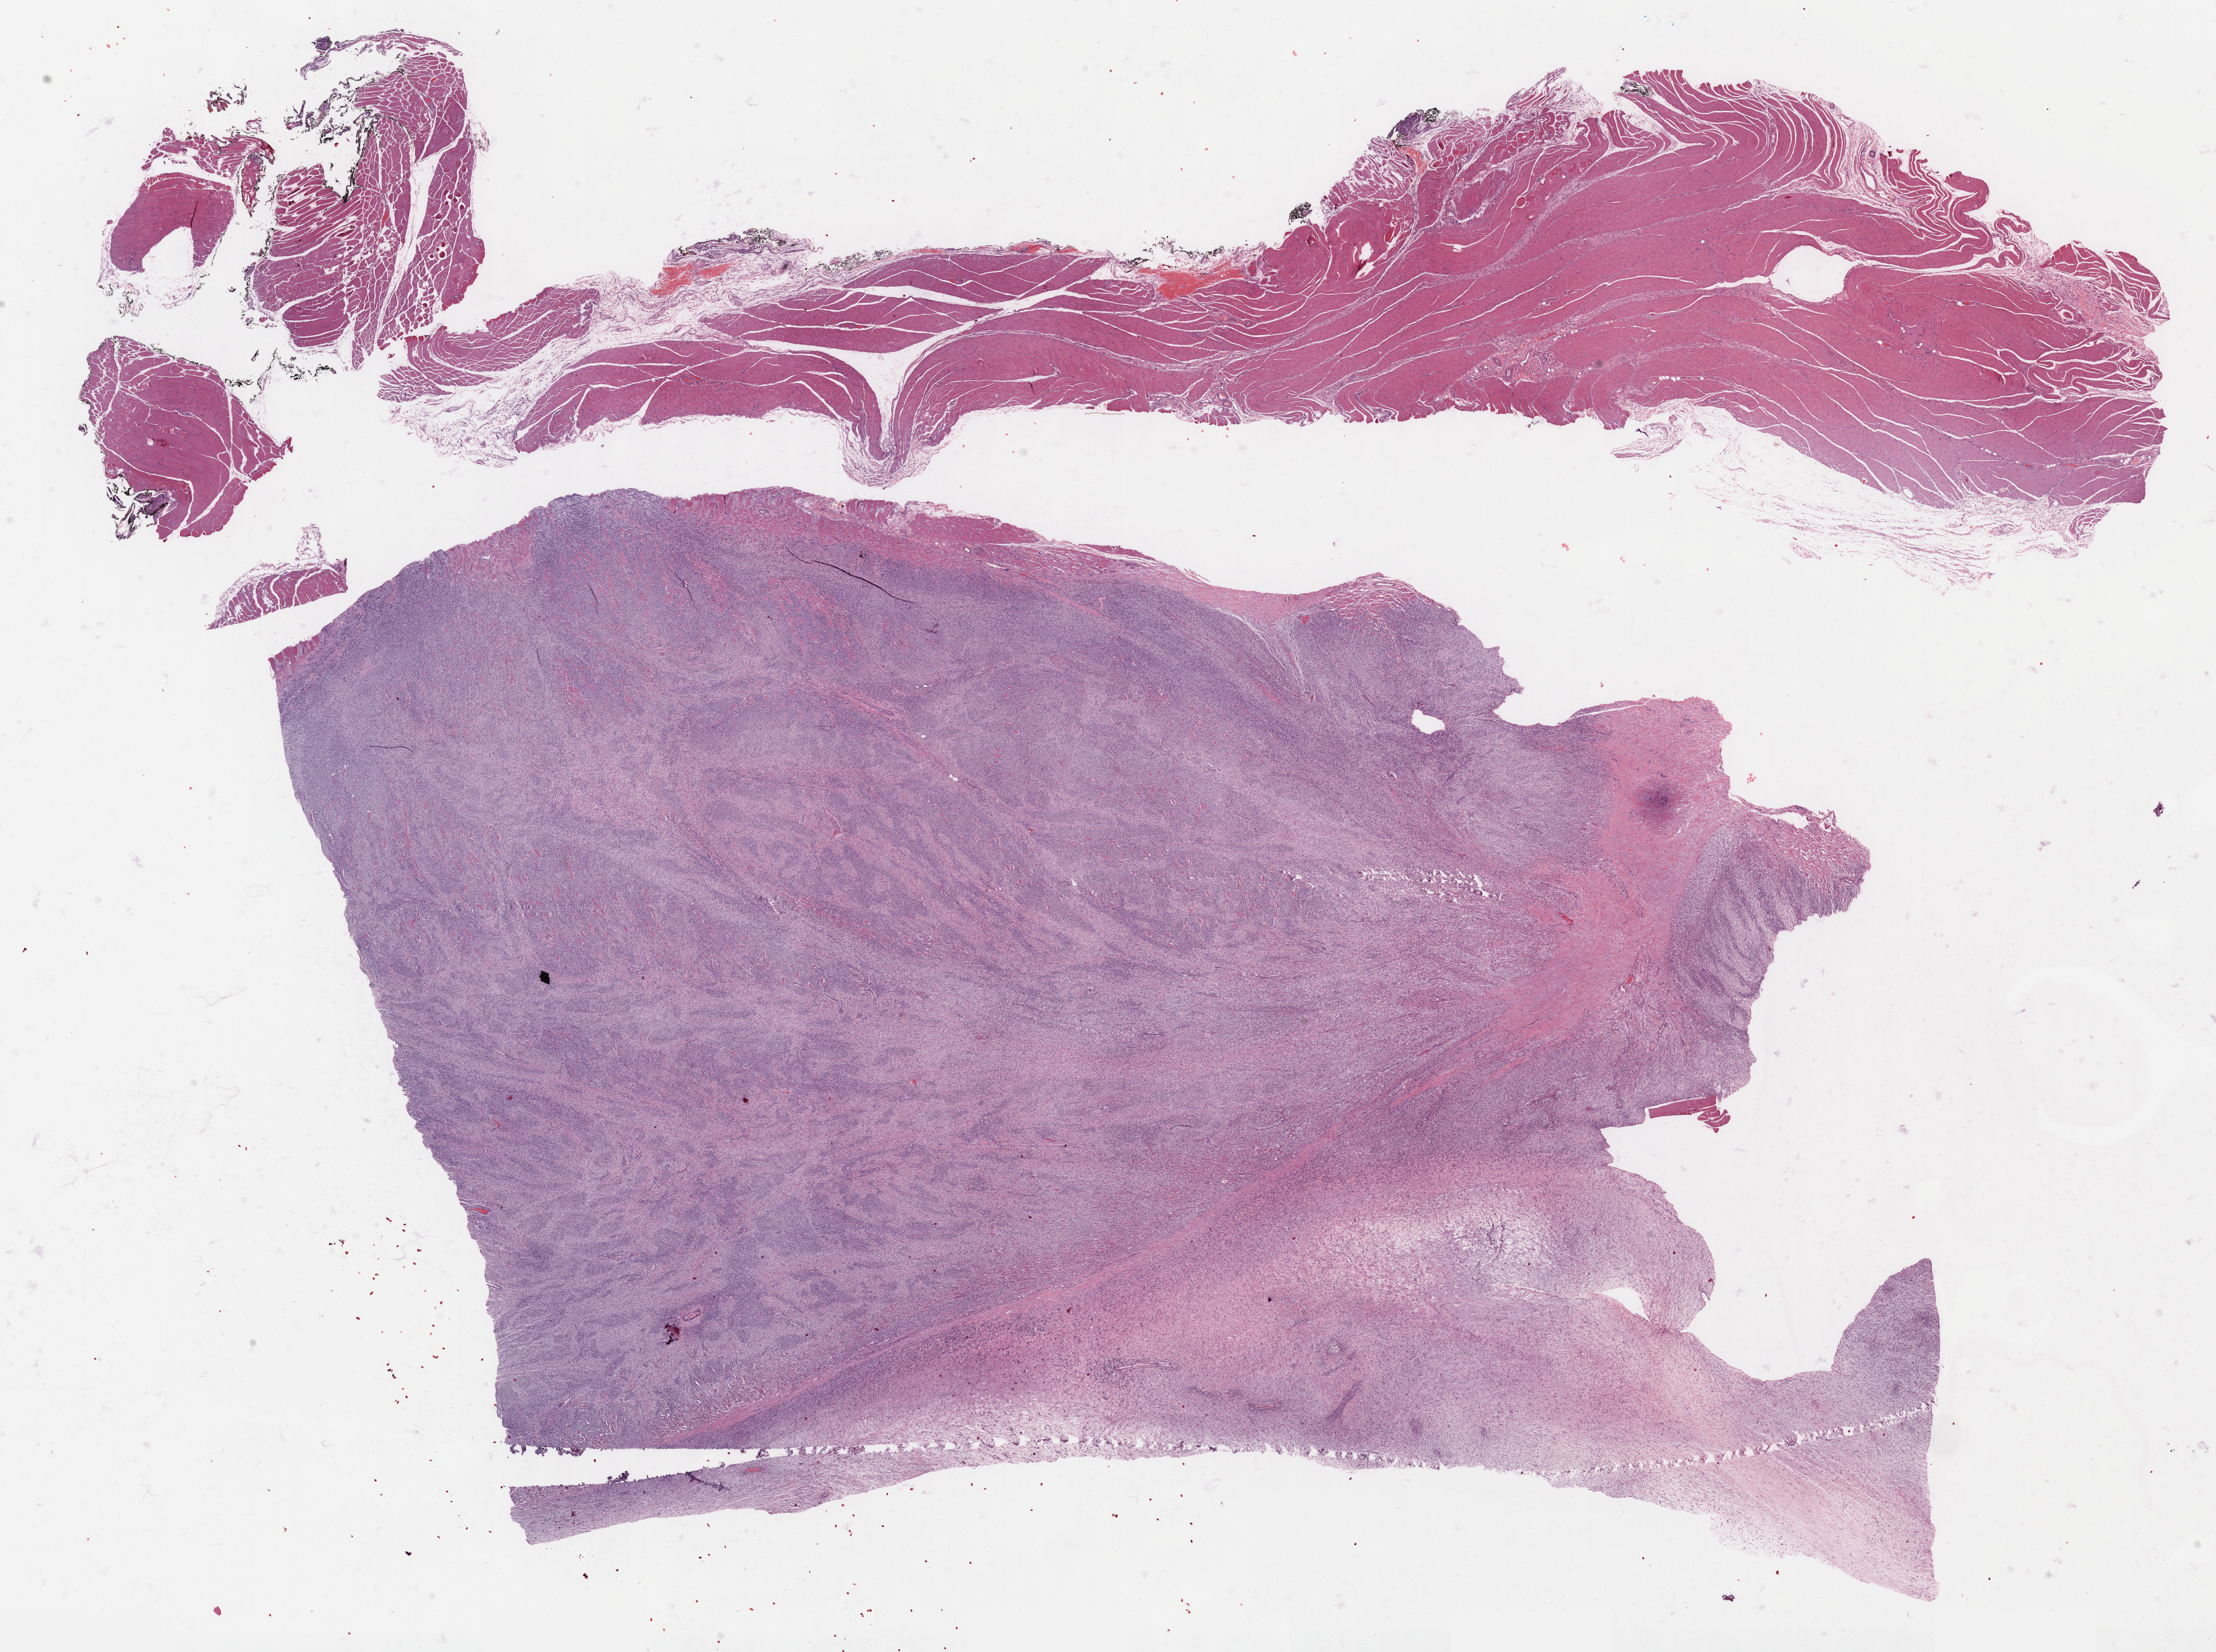
Hematoxylin and eosin (H&E) stained whole-slide image, shown as a low-resolution overview of the whole scanned area (about 26.7 x 19.9 mm). FFPE section. Sample: primary tumour, connective, subcutaneous and other soft tissues. Female, age 53 years at initial diagnosis.
Pathologic diagnosis: Fibromyxosarcoma (connective, subcutaneous and other soft tissues of lower limb and hip).